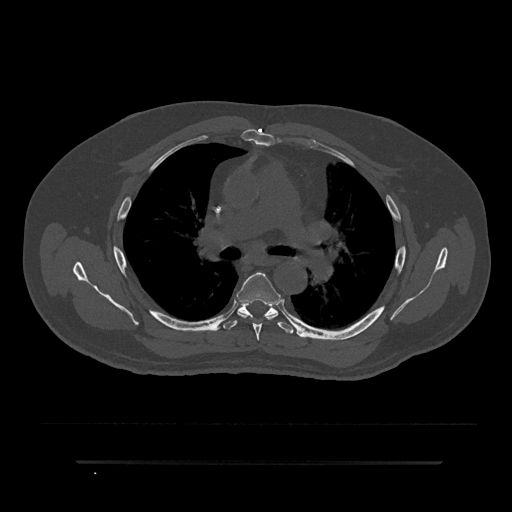
CT including the spine, one axial slice. 120 kVp. Bone window (W 1800 / L 400 HU). 0.5 mm slice thickness. 512 × 512 image matrix, field of view 464 × 464 mm. Patient: male, 59 years. From the clinical record (not read from this slice): primary cancer: bile ducts; vertebrae with lytic lesions (as recorded): T10.
Outlined on this slice (semi-automatic segmentation, software-assisted and operator-edited):
- T5 vertebra: box from (x=237, y=272) to (x=278, y=341) px
- T6 vertebra: (x=223, y=300)–(x=294, y=334)